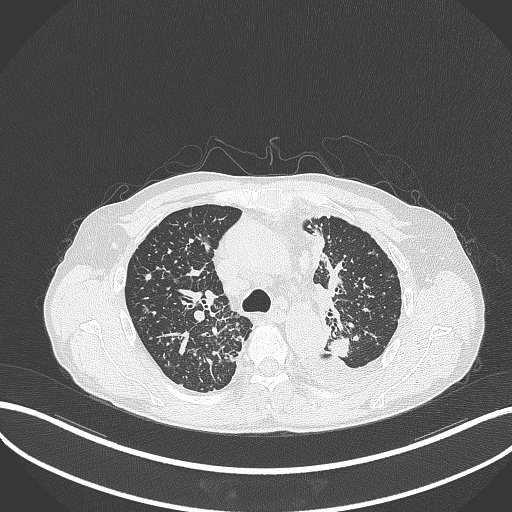
Chest CT, one axial slice. Position 251 of 325 along the scan axis. Reconstruction kernel B70f. Lung window (W 1500 / L -600 HU). 1 mm slice thickness. 512 × 512 image matrix, field of view 400 × 400 mm. Male patient, age 58 years. From the clinical record (not read from this slice): clinical TNM (as recorded): T1c N3 M1.
Outlined on this slice (rectangle marked by the reading radiologist):
- lung tumour (recorded histology: adenocarcinoma): bounding box [x1, y1, x2, y2] px = [323, 332, 355, 362]